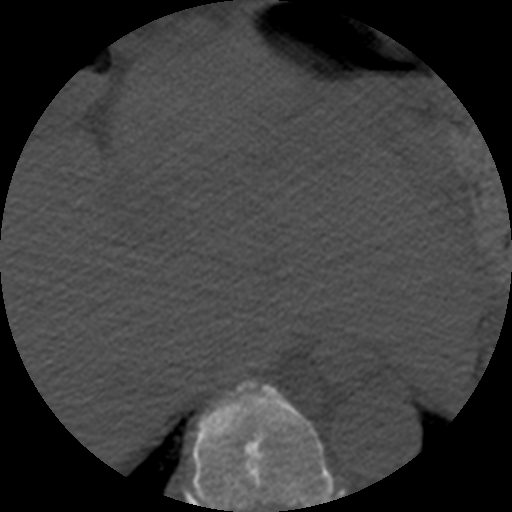
CT including the spine, one axial slice; position 281 of 508 along the scan axis; bone window (W 1800 / L 400 HU); 1.25 mm slice thickness; 512 × 512 image matrix, field of view 160 × 160 mm. Patient age 57 years. From the clinical record (not read from this slice): primary cancer: prostate.
Outlined on this slice (semi-automatic segmentation, software-assisted and operator-edited):
- T9 vertebra: bounding box [x1, y1, x2, y2] px = [184, 380, 346, 512]